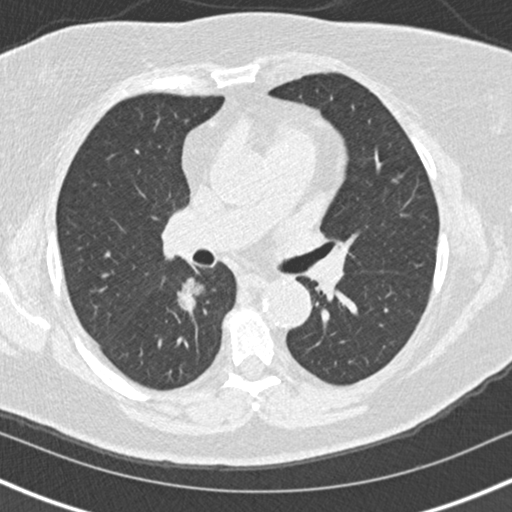
Low-dose screening chest CT, one axial slice. Position 90 of 152 along the scan axis. 120 kVp. Lung window (W 1500 / L -600 HU). 512 × 512 image matrix.
Structures marked on this image (outlined manually by an expert reader):
- lesion 1 (tumor, lower lobe of right lung): bounding box <177,278,204,311> (left, top, right, bottom; pixels)